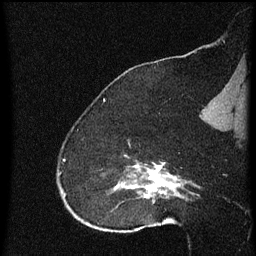
Breast MRI (dynamic contrast-enhanced), one sagittal slice; slice 44 of 60 in the series (ordered by position); dynamic contrast-enhanced series, image 2 of 4 at this slice position (ordered by acquisition); 1.5 T; TE 4.2 ms, TR 8 ms; 2 mm slice thickness; 256 × 256 image matrix, field of view 180 × 180 mm. Female patient, age 52 years.
Structures marked on this image (semi-automatically segmented with operator editing):
- analysis volume of interest (the breast-tissue region the enhancement analysis was run in; not a lesion): box from (x=73, y=154) to (x=172, y=219) px
- tumour enhancement mask (voxels above the 70 % enhancement threshold inside the analysis volume of interest): (x=117, y=162)–(x=172, y=199)